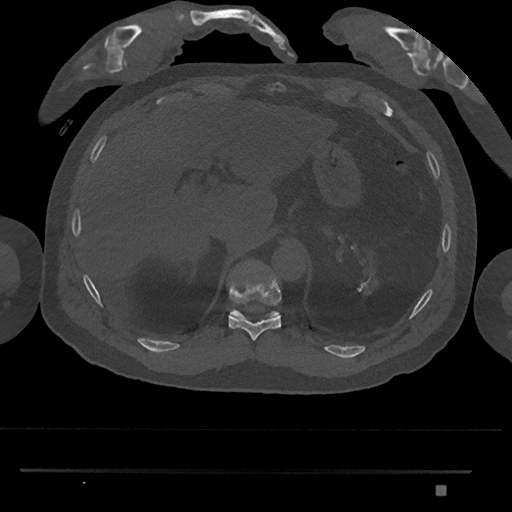
CT including the spine, one axial slice. Position 989 of 1134 along the scan axis. Reconstruction kernel Br40s/3. Bone window (W 1800 / L 400 HU). 0.5 mm slice thickness. 512 × 512 image matrix, field of view 429 × 429 mm. Male patient, age 65 years. From the clinical record (not read from this slice): primary cancer: prostate.
Annotated regions visible in this slice (semi-automatic segmentation, software-assisted and operator-edited):
- T10 vertebra: box from (x=228, y=267) to (x=282, y=341) px
- T11 vertebra: (x=230, y=309)–(x=280, y=319)